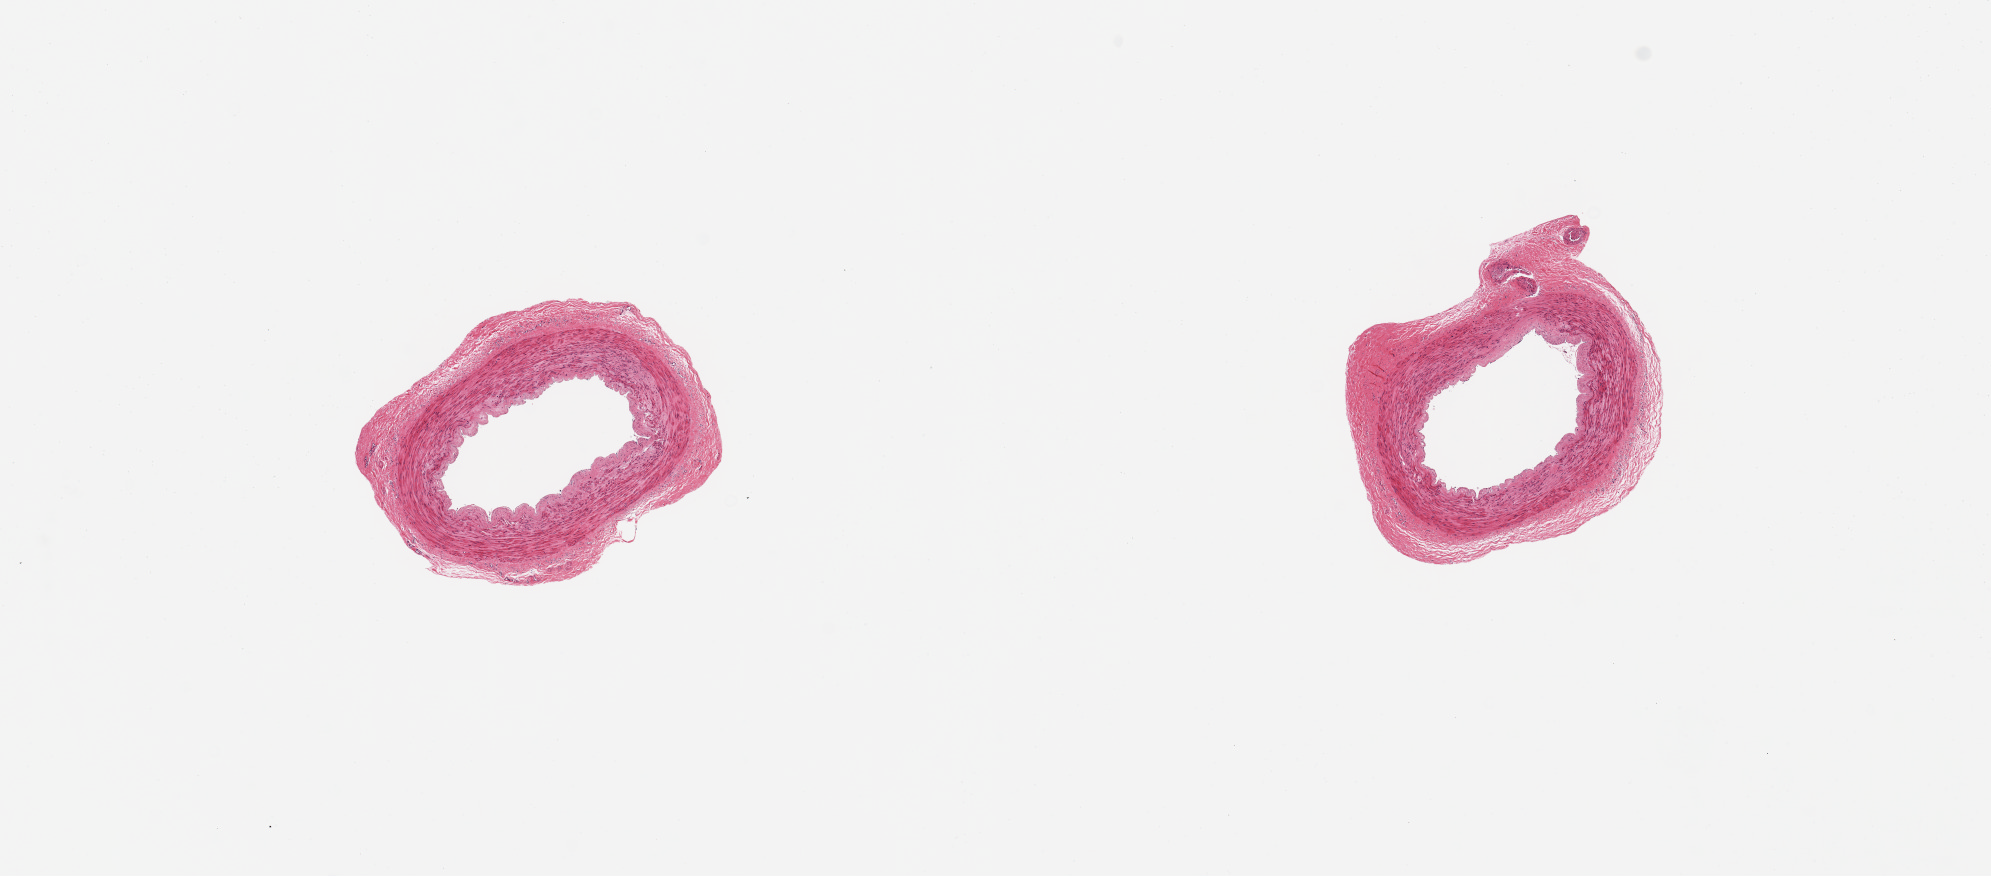
H&E whole-slide image, brightfield, low-resolution overview of the scanned area, about 15.8 x 6.9 mm (from a 20x scan), PAXgene-fixed, paraffin-embedded tissue, section of tibial artery (target tissue), tissue donor sample. Donor sex: male.
• reviewer comment on this tissue sample: 2 pieces; no plaques